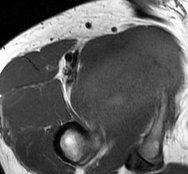
MRI of an extremity soft-tissue mass, one axial slice; slice 61 of 93 in the series (ordered by position); MR volume resampled by the dataset authors to the PET/CT grid (not the native acquisition matrix); 3.27 mm slice thickness; 188 × 174 image matrix, field of view 184 × 170 mm. Male patient. Case-level facts recorded for this patient, not image findings: histological type: undifferentiated - pleiomorphic; grade: high; site of the primary tumour: right thigh.
Outlined on this slice (expert contour drawn on MRI and transferred to this co-registered scan by the dataset authors):
- gross tumour volume including surrounding oedema: bounding box [x1, y1, x2, y2] px = [82, 30, 181, 130]
- gross tumour volume (mass): [82, 30, 181, 130]